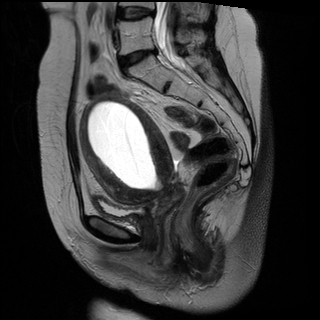
Pelvic MRI for cervical cancer, one sagittal slice; slice 16 of 29 in the series (ordered by position); T2-weighted; 1.5 T; TE 89 ms, TR 2930 ms; 4 mm slice thickness; 320 × 320 image matrix. Female patient, age 49 years.
Structures marked on this image (expert manual segmentation):
- uterus and cervix: bounding box [x1, y1, x2, y2] px = [80, 92, 184, 227]